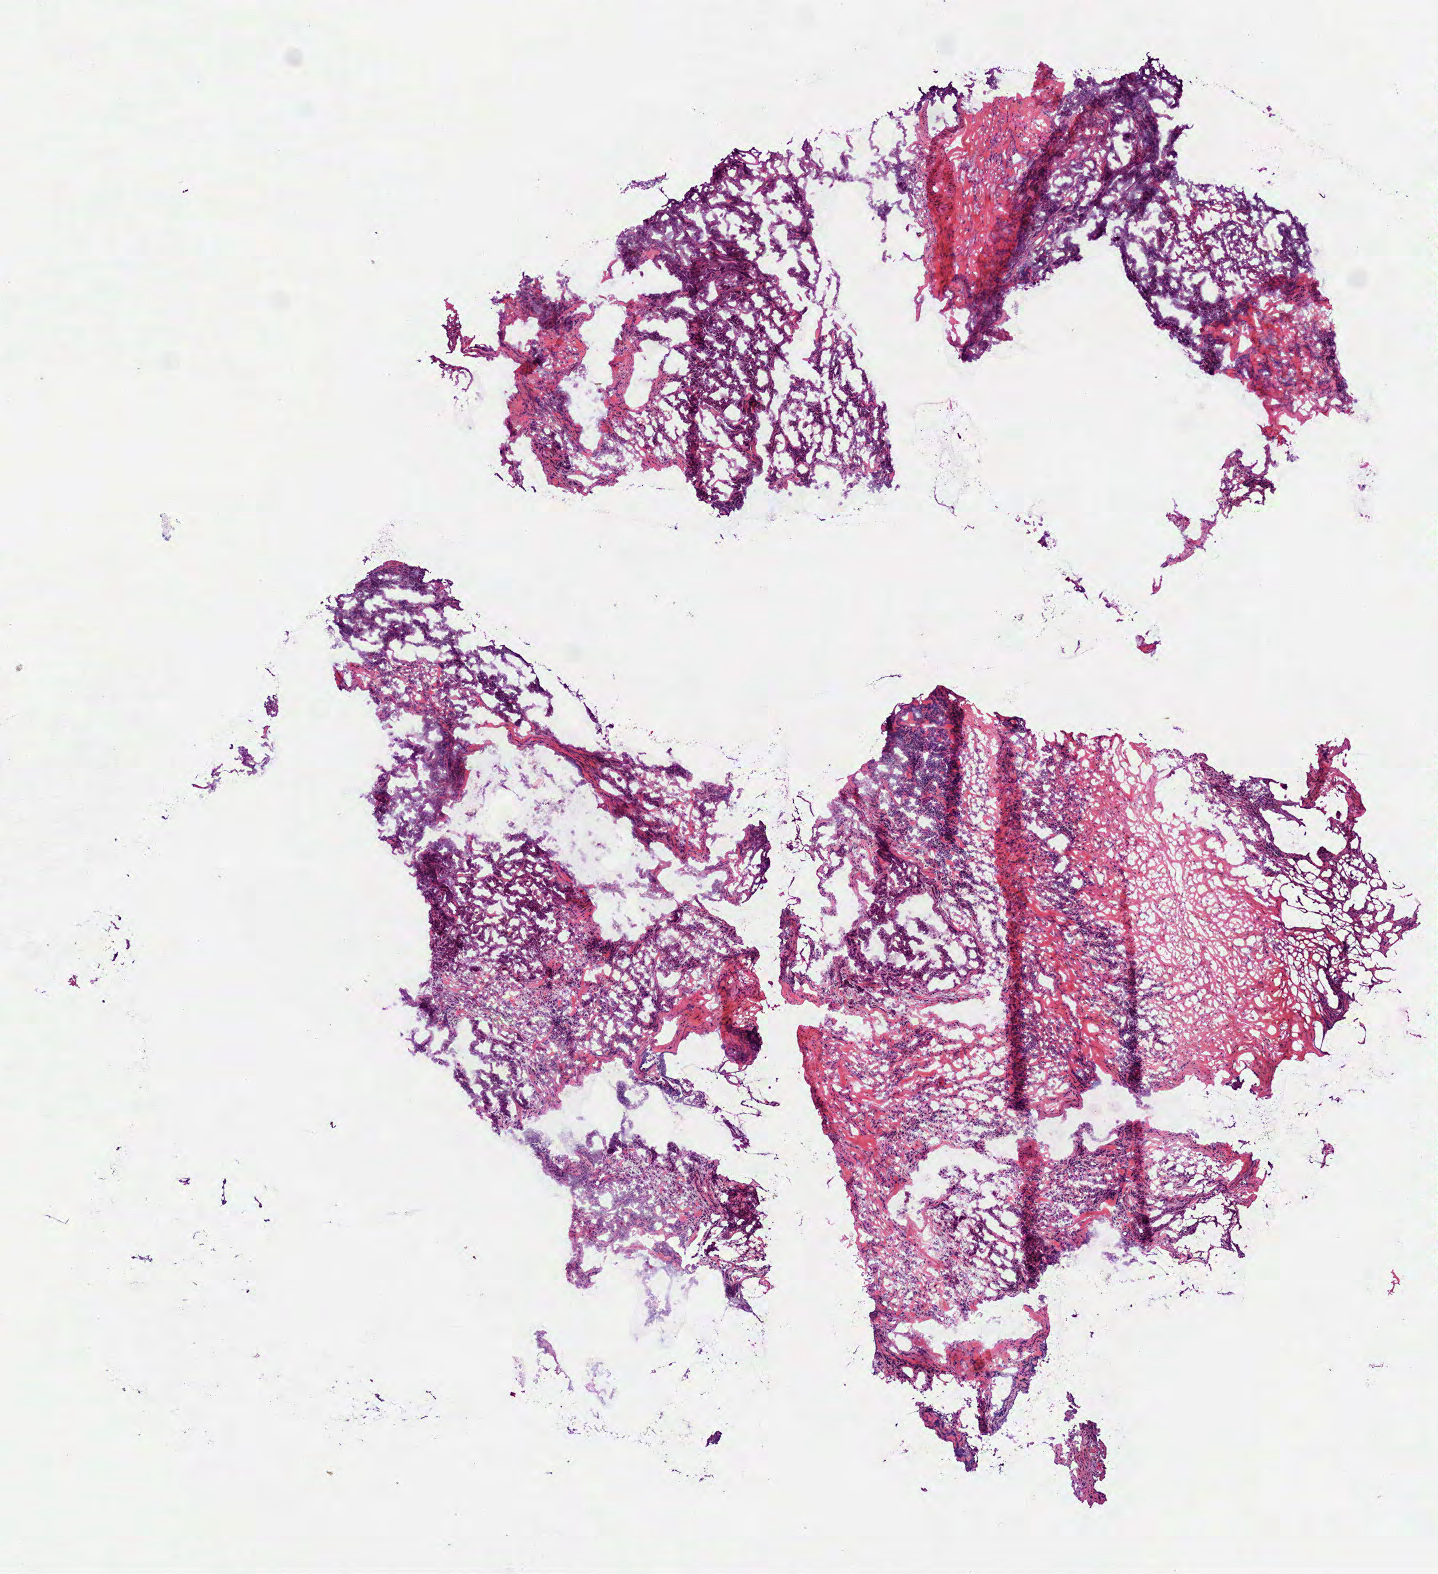
Whole-slide histology image, Hematoxylin and eosin (H&E) stained — whole scanned area (about 5.8 x 6.3 mm) shown as a low-resolution overview. Frozen section. Head and neck, primary tumour sample. Male patient; age at initial diagnosis 55 years. Histologic grade: G3 (poorly differentiated). Pathologist review of this section (percent, as recorded): tumour cells 75%, tumour nuclei 65%, normal cells 0%, stromal cells 25%, necrosis 0%.
AJCC pathologic stage: II. Histologic diagnosis: Squamous cell carcinoma, NOS (overlapping lesion of lip, oral cavity and pharynx).